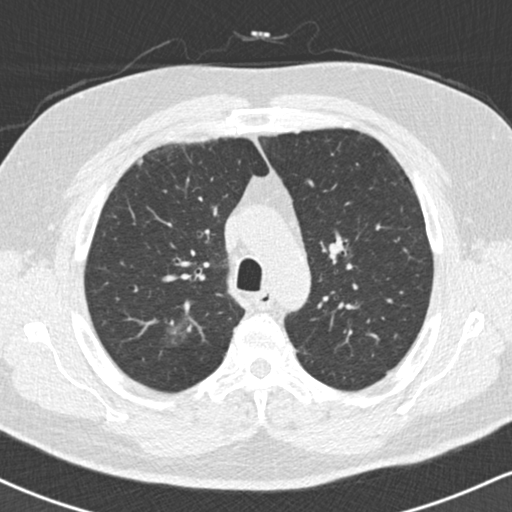
Low-dose screening chest CT, one axial slice. Position 122 of 169 along the scan axis. Reconstruction kernel B30f. 120 kVp. Lung window (W 1500 / L -600 HU). 2 mm slice thickness. 512 × 512 image matrix, field of view 320 × 320 mm.
Annotated regions visible in this slice (outlined manually by an expert reader):
- lesion 1 (tumor, upper lobe of right lung): bounding box <165,321,190,348> (left, top, right, bottom; pixels)